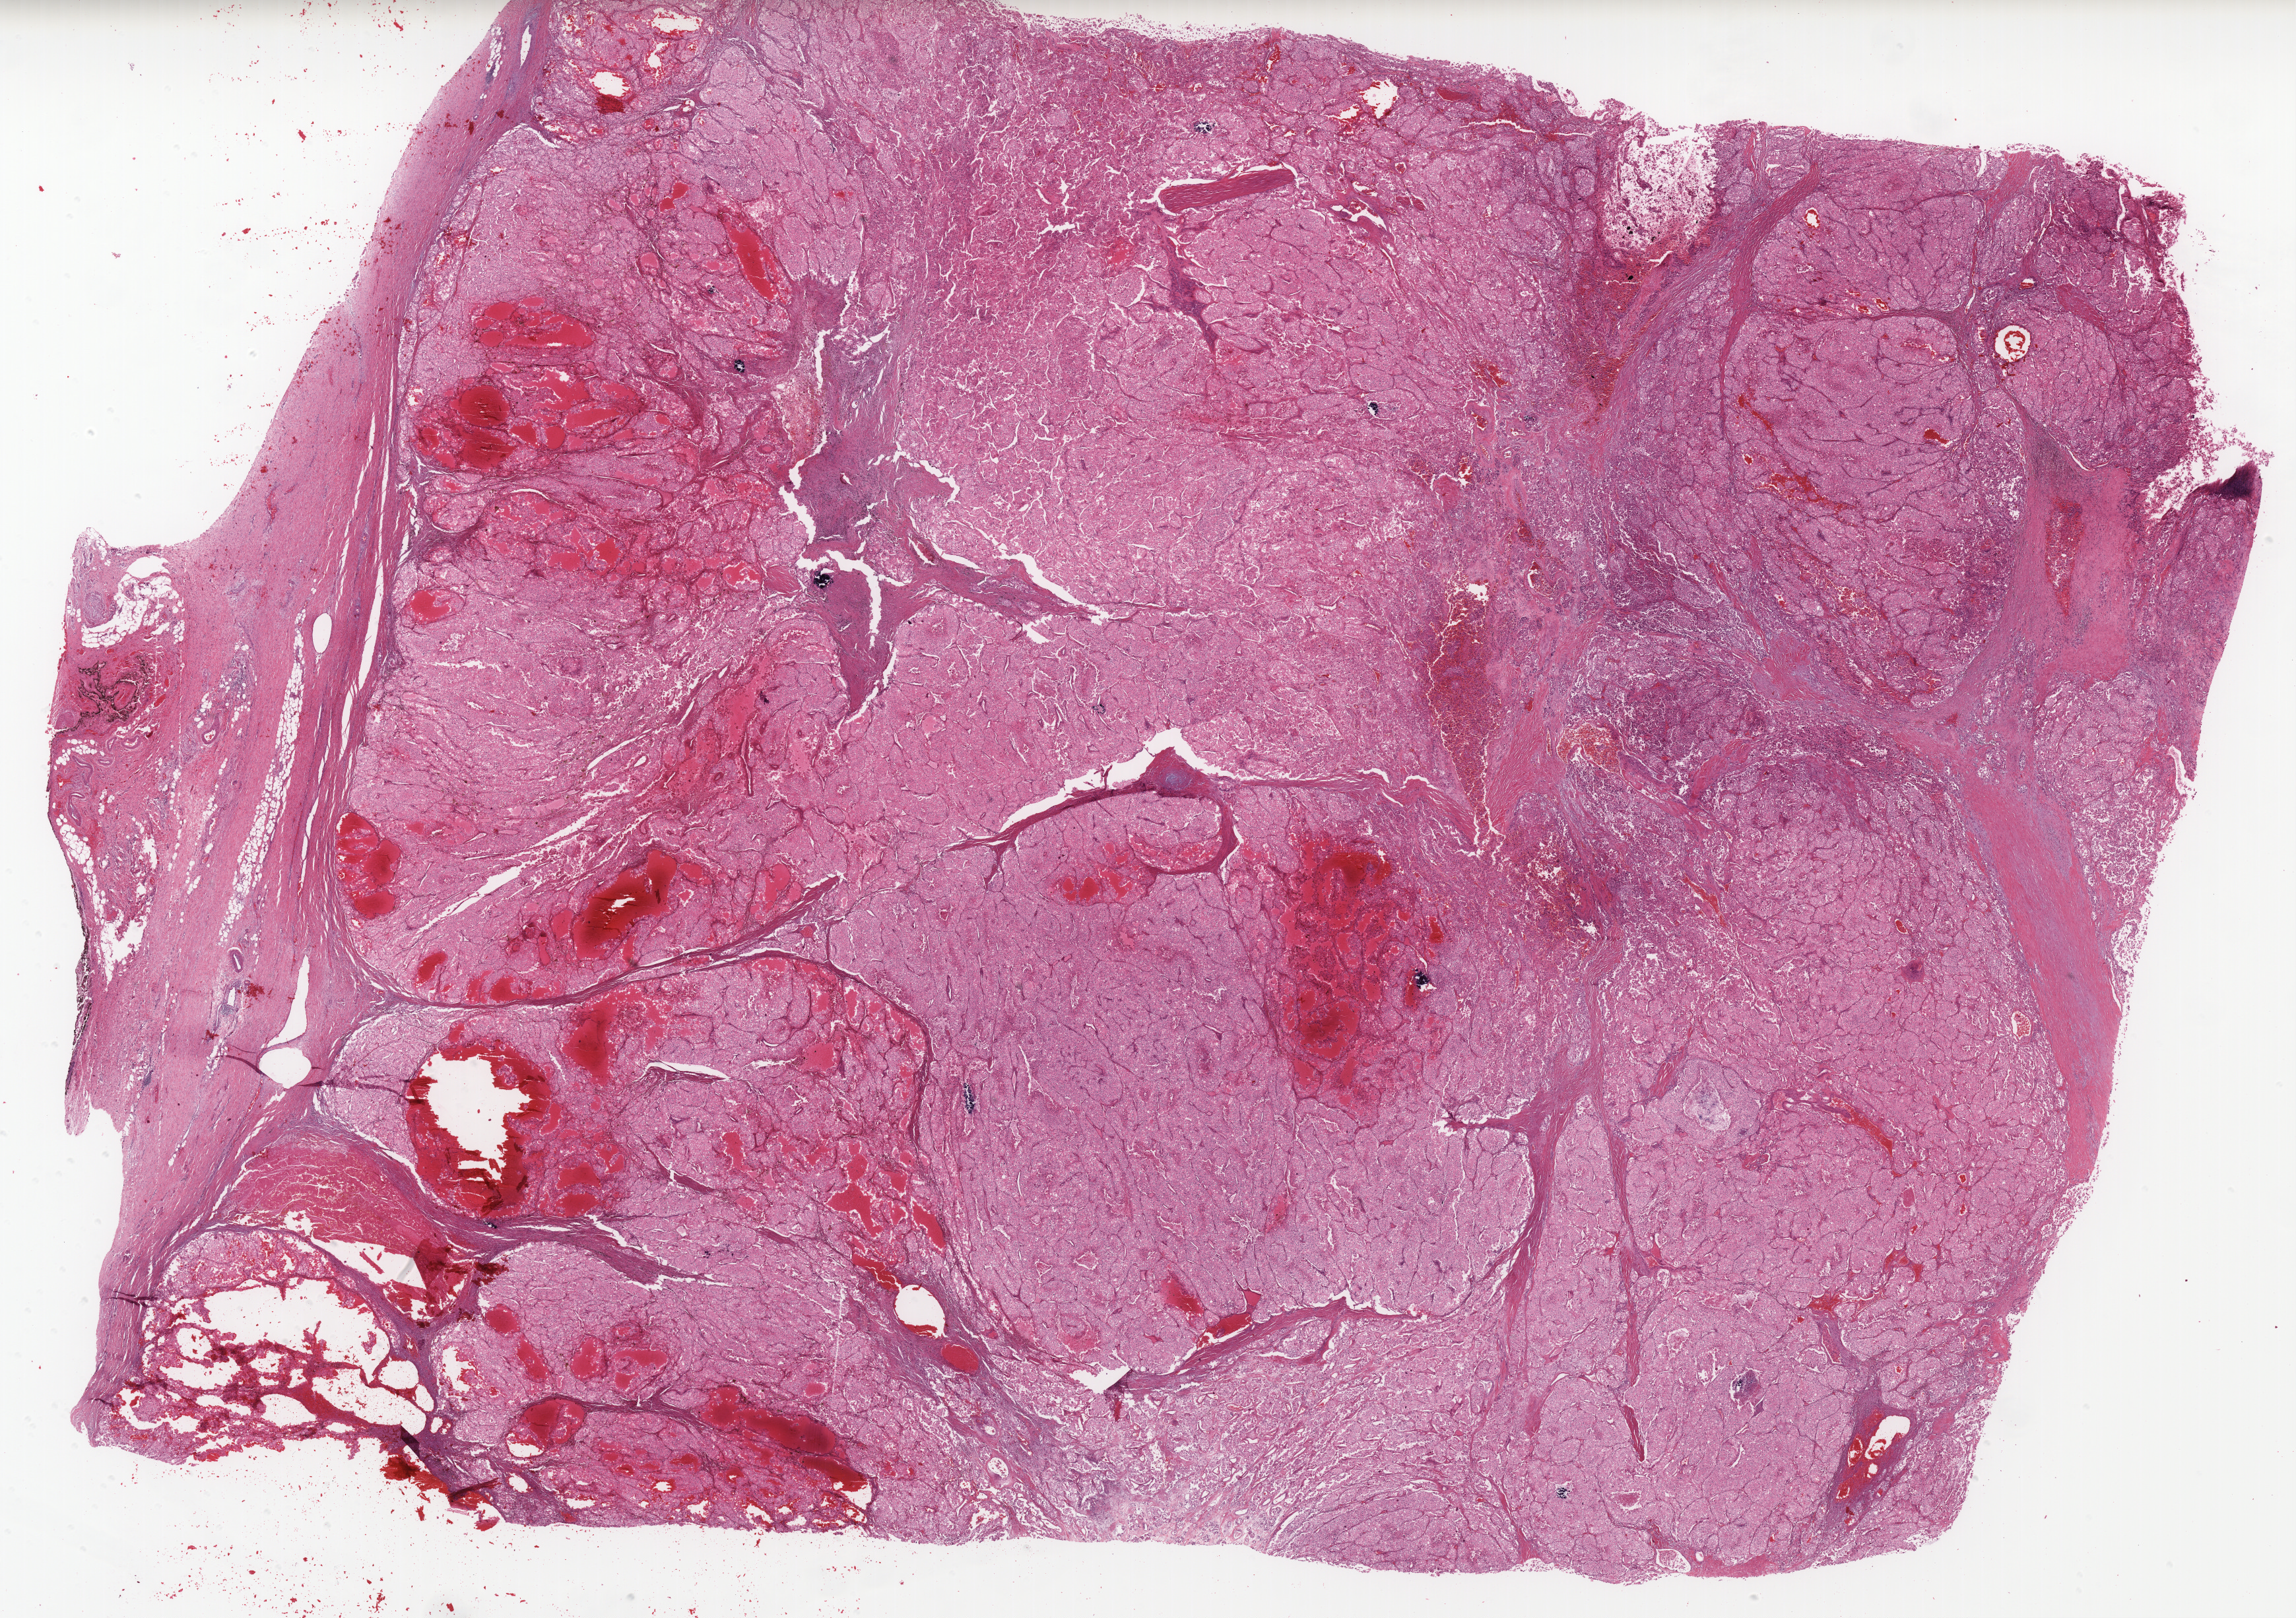
Digitized Hematoxylin and eosin (H&E) stained tissue section (whole slide) — a low-resolution overview of the entire scanned area, about 27.8 x 19.6 mm (from a 40x scan); FFPE section; sample: primary tumour, kidney. Patient: male, age at initial diagnosis 67 years.
- lymph nodes positive (case pathology): 1 of 33 examined
- TNM: T3a N1 M1
- AJCC pathologic stage: IV
- laterality: left
- diagnosis: Renal cell carcinoma, chromophobe type